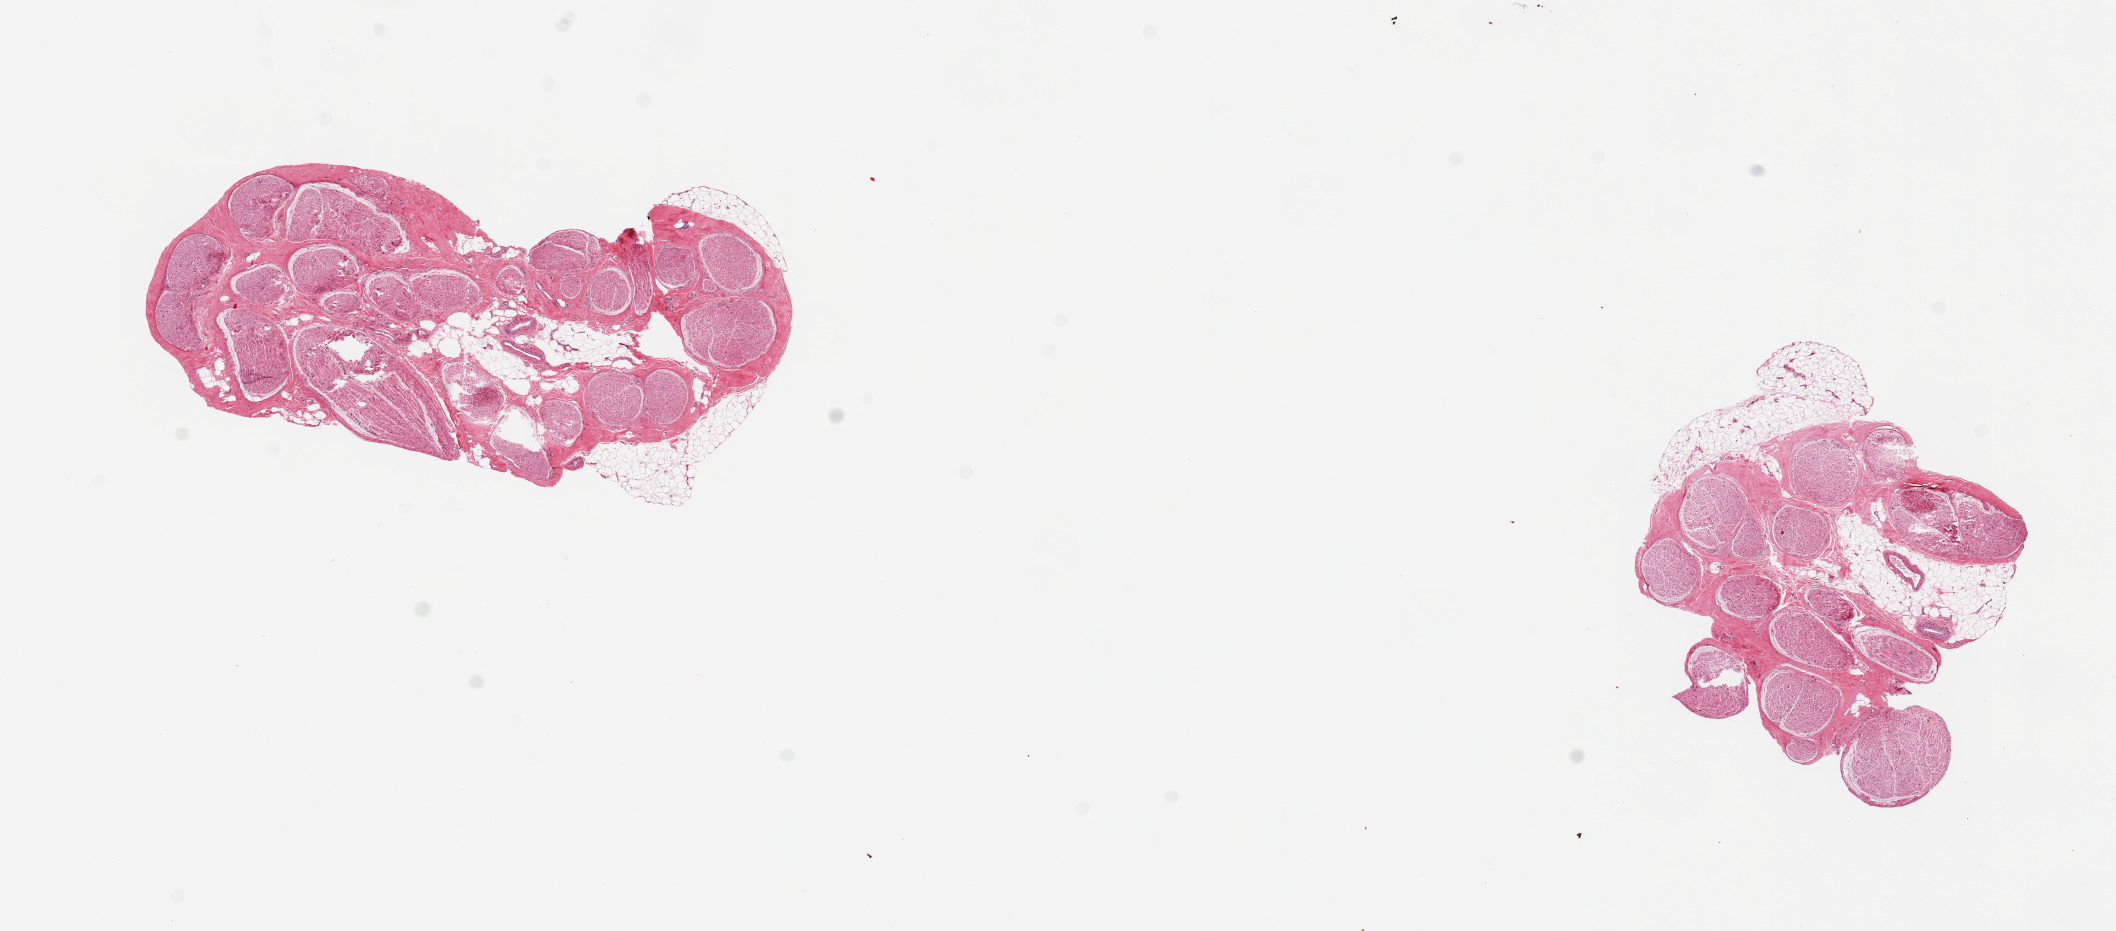
Haematoxylin and eosin whole-slide image, a low-resolution overview of the entire scanned area, about 16.7 x 7.4 mm (from a 20x scan), PAXgene-fixed paraffin-embedded (PFPE) section, sampled site (target tissue): tibial nerve, tissue donor sample.
Reviewer comment on this tissue sample: 2 pieces, generally clean specimens, nubbin of ahderent fat up to ~0.5mm.